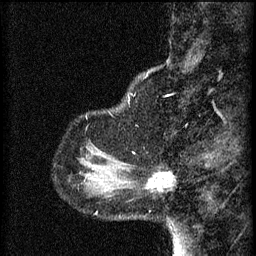
Breast MRI (dynamic contrast-enhanced), one sagittal slice; position 11 of 60 along the scan axis; 3 images stored at this slice position (order not interpretable as contrast timing); 1.5 T; TE 4.2 ms, TR 8.2 ms; 2 mm slice thickness; 256 × 256 image matrix, field of view 180 × 180 mm. Female patient, age 37 years.
Annotated regions visible in this slice (semi-automatic segmentation, software-assisted and operator-edited):
- analysis volume of interest (the breast-tissue region the enhancement analysis was run in; not a lesion): bounding box (x1, y1, x2, y2) in pixels: (126, 166, 174, 193)
- tumour enhancement mask (voxels above the 70 % enhancement threshold inside the analysis volume of interest): (148, 172, 173, 191)